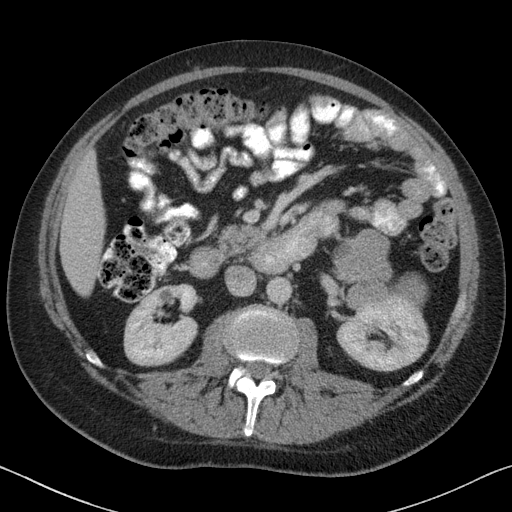
Contrast-enhanced abdominal CT, one axial slice. Reconstruction kernel B31f. 120 kVp. Soft-tissue window (W 400 / L 40 HU). 3 mm slice thickness. 512 × 512 image matrix, field of view 366 × 366 mm. Patient: male, 51 years. From the clinical record (not read from this slice): diagnosis: adrenocortical carcinoma; tumour side: left adrenal; tumour size at pathology: 16.5 cm.
Annotated regions visible in this slice (semi-automatically segmented with operator editing):
- mass: box from (x=334, y=231) to (x=425, y=306) px